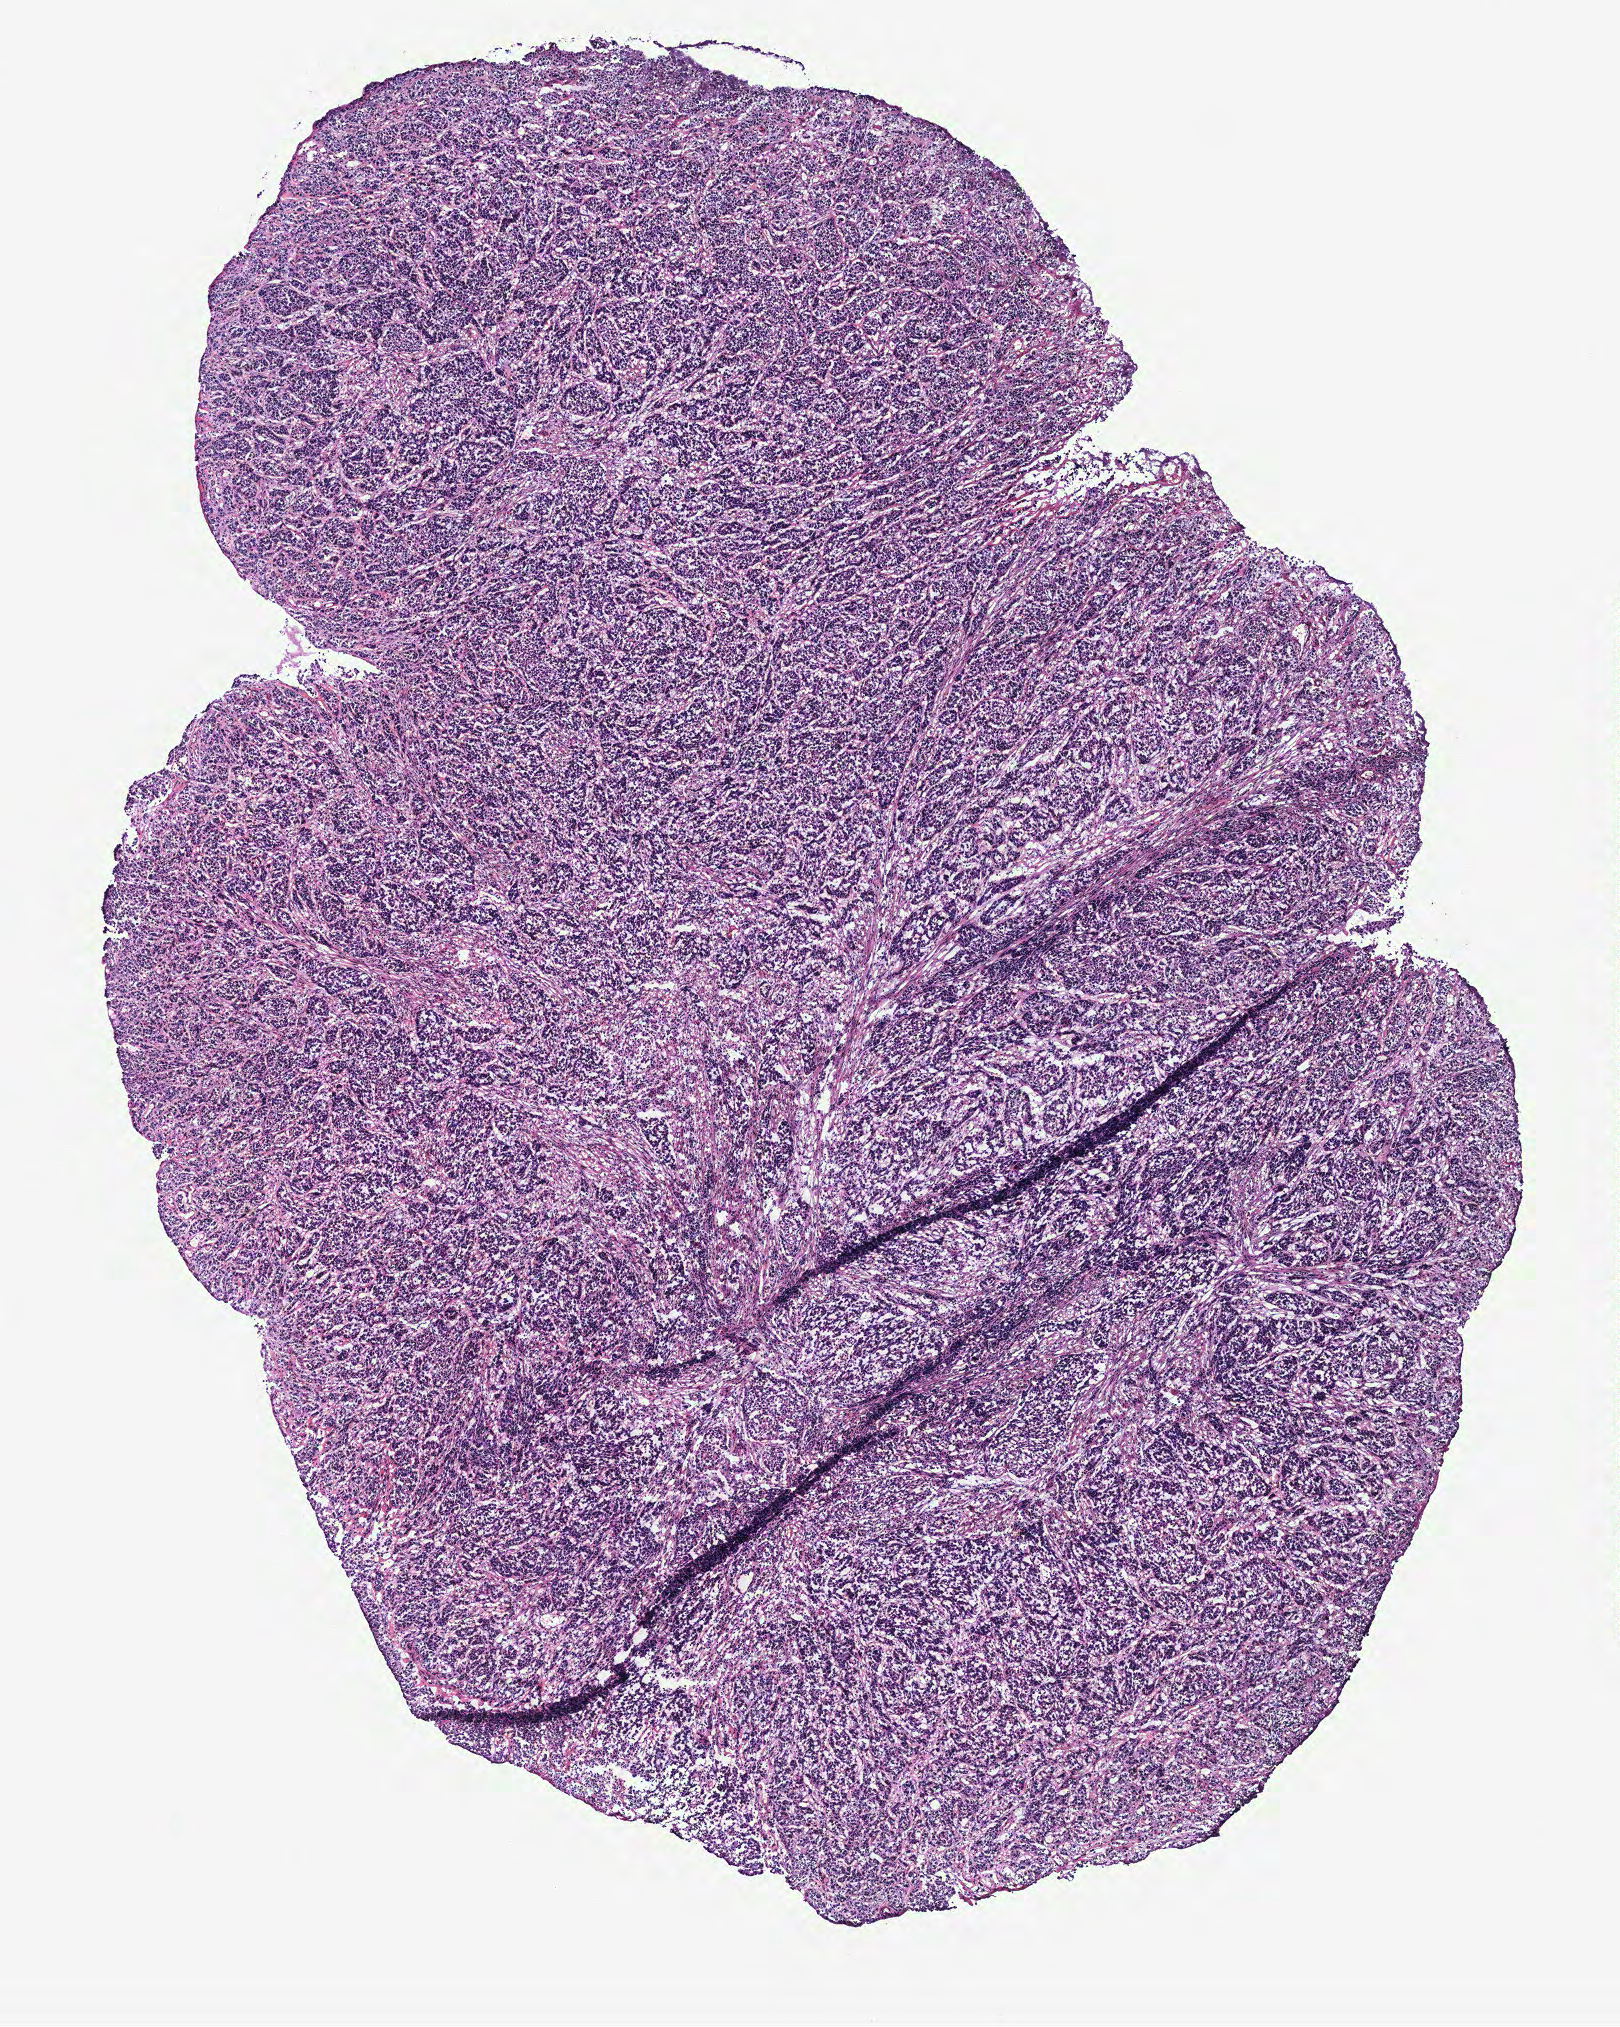
H&E whole-slide image, shown as a low-resolution overview of the whole scanned area (about 6.5 x 8.1 mm, slide scanned at 40x), colon, tissue type not recorded. Patient sex: female.
Patient diagnosis: Adenocarcinoma, NOS.